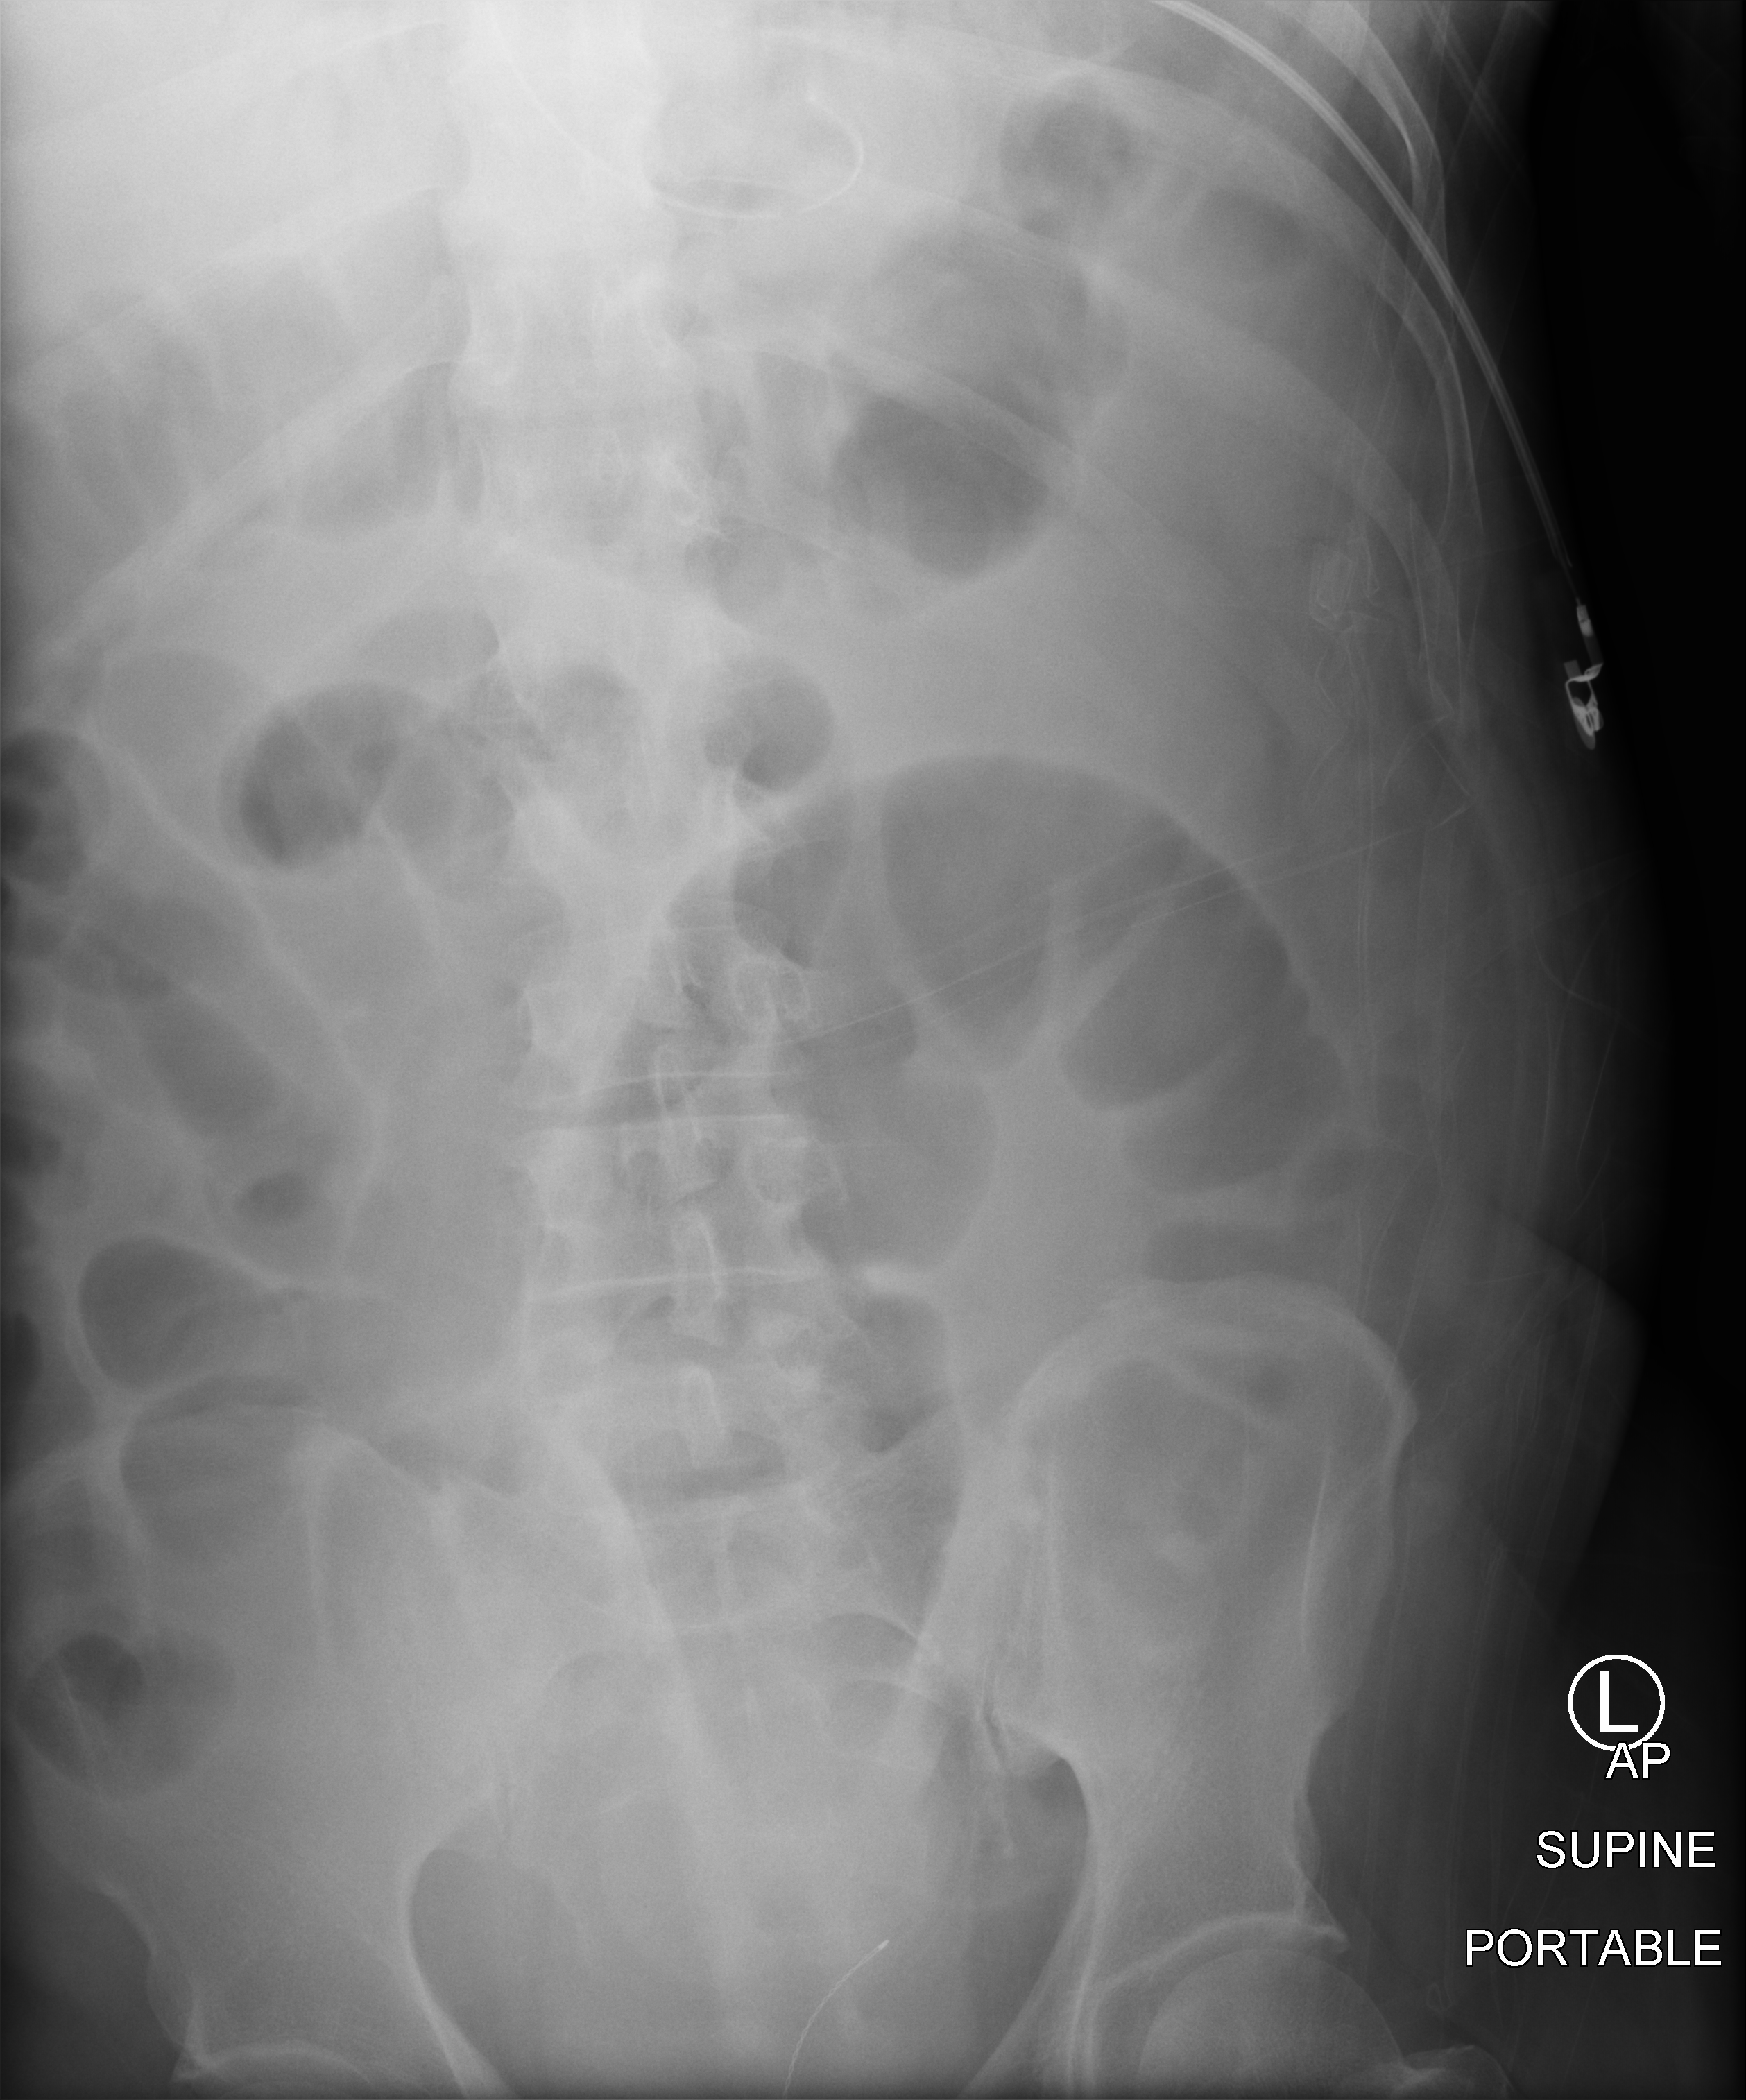
Abdomen X-ray (portable); anteroposterior (AP) projection. Patient hospitalised with COVID-19; male, aged 18–59 years.
Hospital-stay facts (about this admission, not read from this image; timing relative to this image not recorded): admitted to intensive care during this hospital stay: yes; mechanically ventilated during this hospital stay: yes; diabetes (admission record): yes.